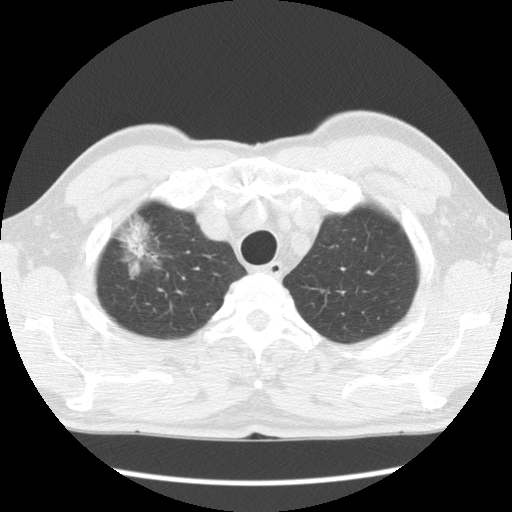
Chest CT (low-dose screening protocol), one axial image, first (baseline) screen, lung window (W 1500 / L -600 HU). Male, age 64 years at enrolment. Former smoker at enrolment.
Expert-annotated lung lesion, bounding box <104,211,173,280> (left, top, right, bottom; pixels). The screening reader recorded 2 non-calcified nodules or masses ≥4 mm on this exam (right upper lobe, left upper lobe); which of them this box marks is not recorded. Participant outcome: lung cancer diagnosed 750 days after this screen (after the third annual screen) — adenocarcinoma, NOS, right upper lobe, well differentiated (G1), stage IB (AJCC 6th edition), 45 mm at pathology.